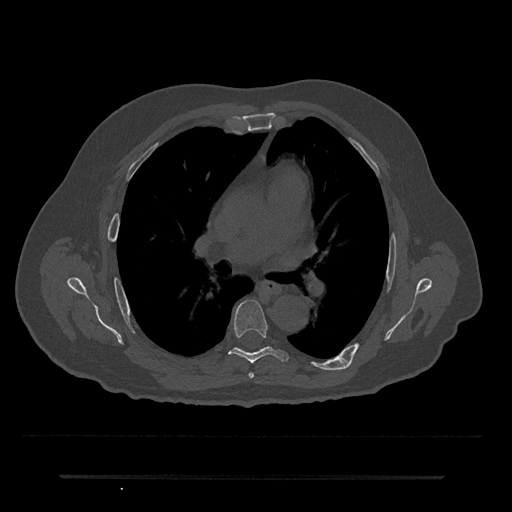
CT including the spine, one axial slice; position 435 of 797 along the scan axis; 120 kVp; bone window (W 1800 / L 400 HU); 0.5 mm slice thickness; 512 × 512 image matrix, field of view 437 × 437 mm. Patient: male, 69 years. From the clinical record (not read from this slice): primary cancer: prostate.
Outlined on this slice (semi-automatically segmented with operator editing):
- T5 vertebra: box from (x=248, y=372) to (x=254, y=379) px
- T6 vertebra: (x=229, y=299)–(x=288, y=364)